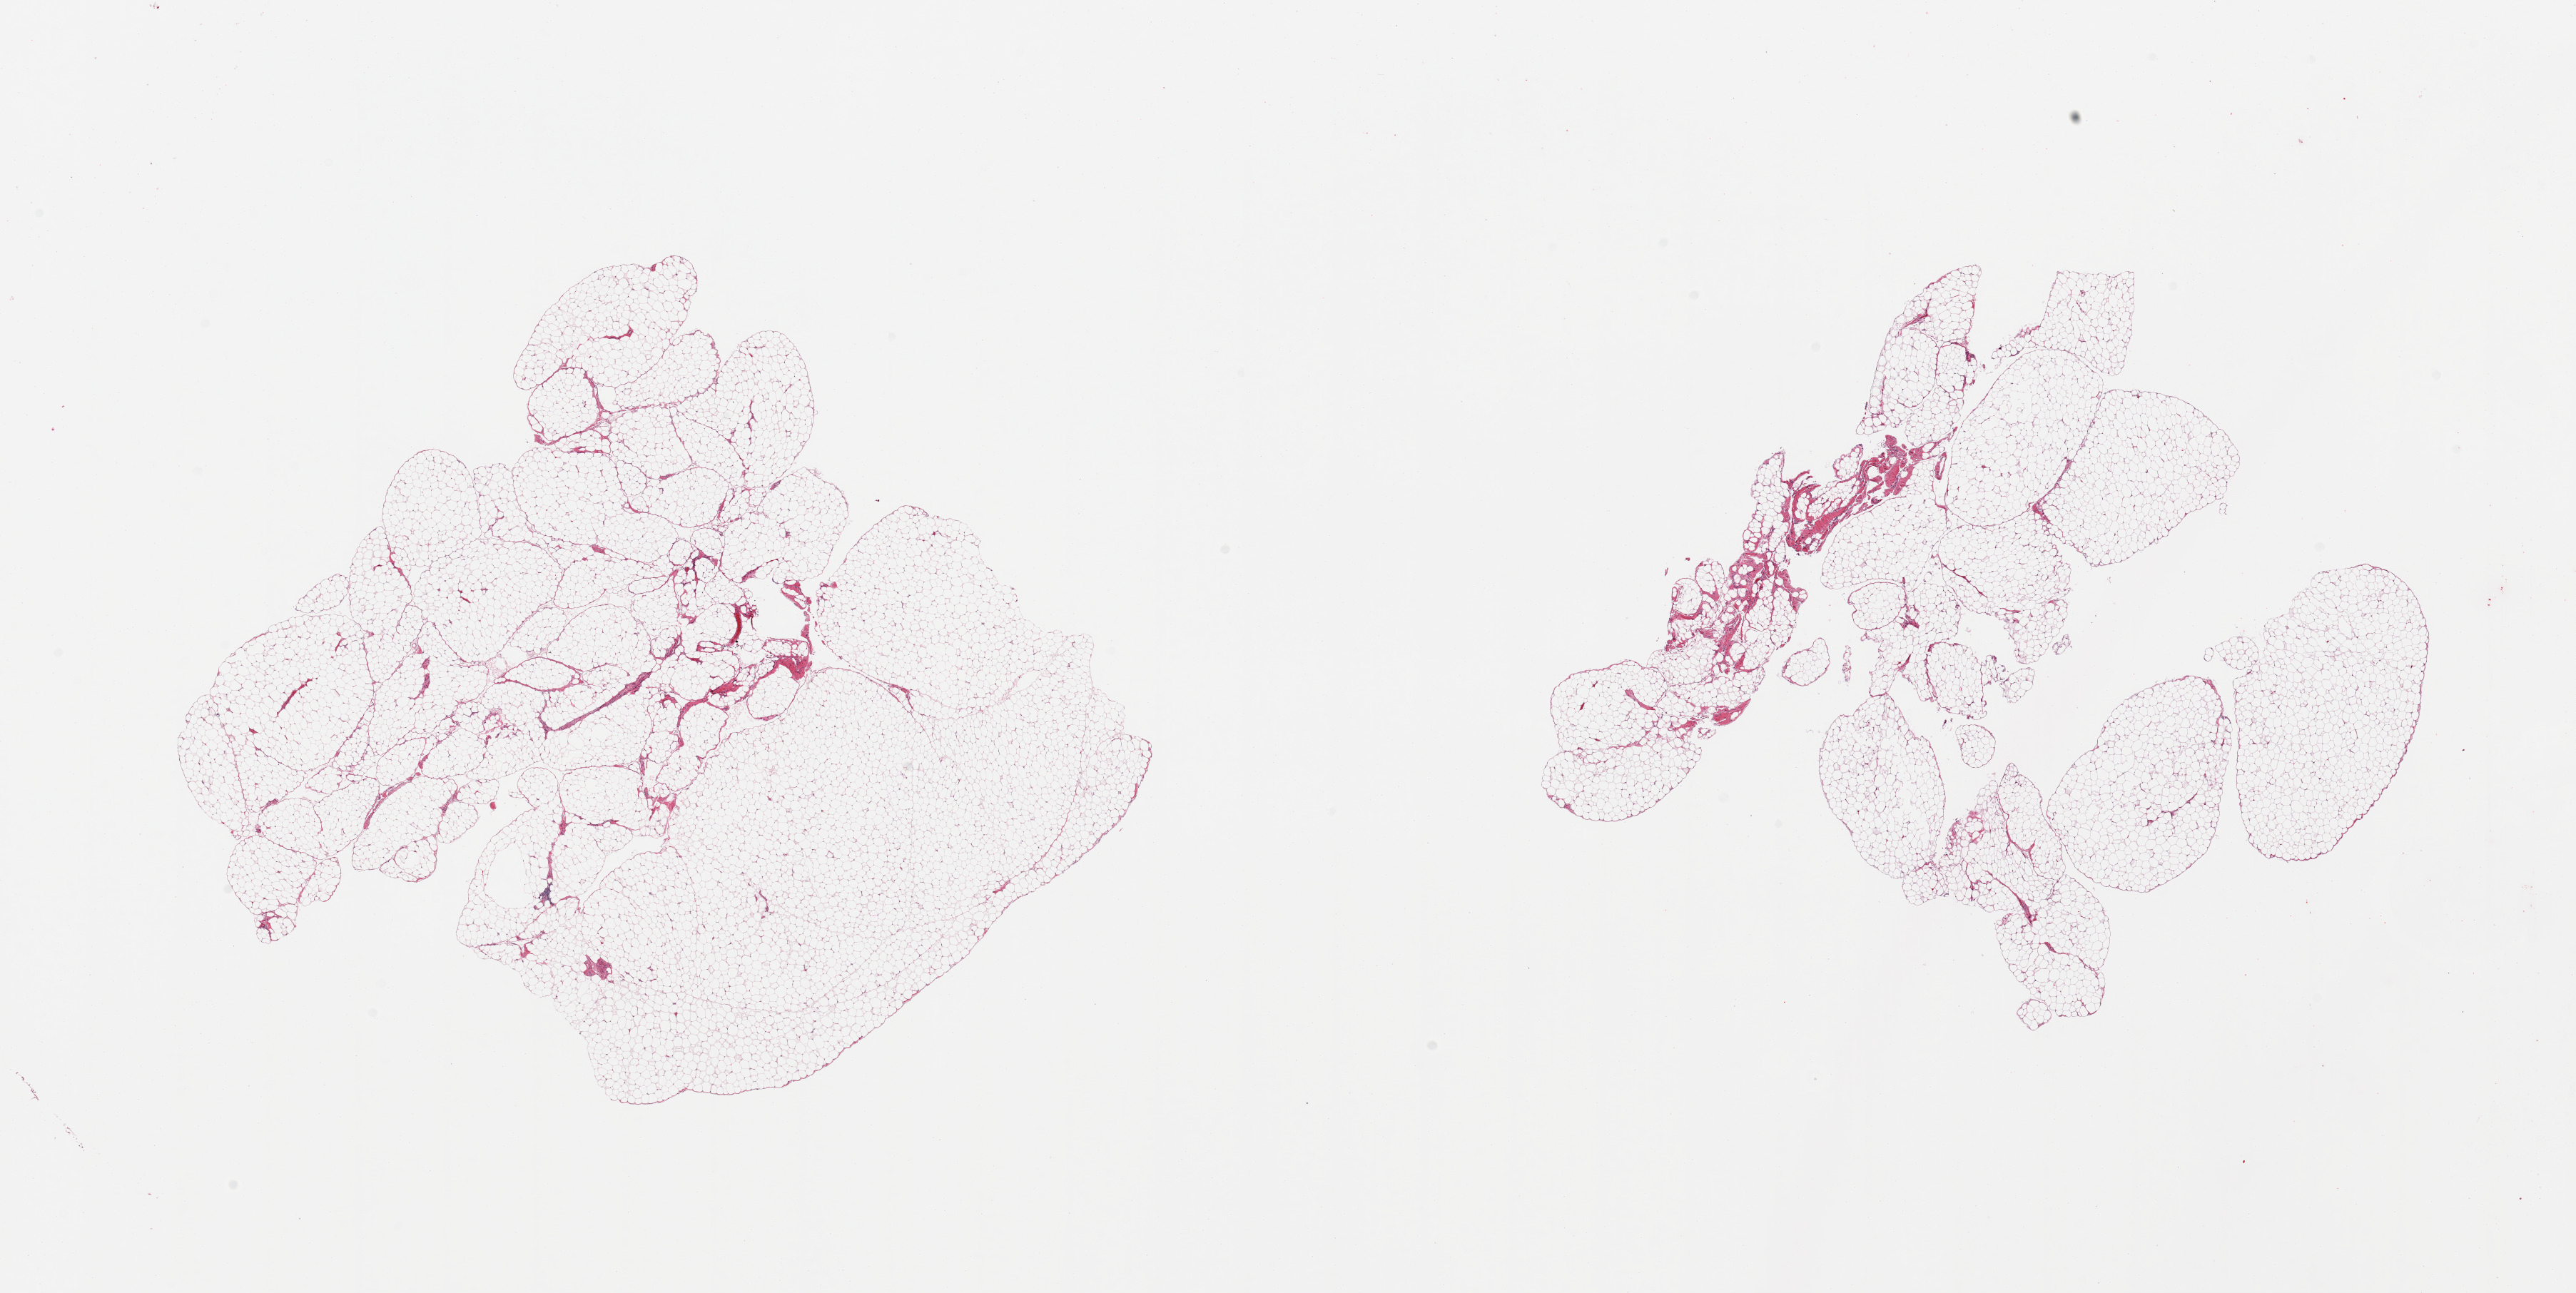
Digitized haematoxylin and eosin-stained section, shown as a low-resolution overview of the whole scanned area (about 28.5 x 14.3 mm); PAXgene-fixed paraffin-embedded (PFPE) section; section of omentum (target tissue); donor tissue sample. Donor sex: male.
Review note (as recorded): 2 pieces <5% fascia.